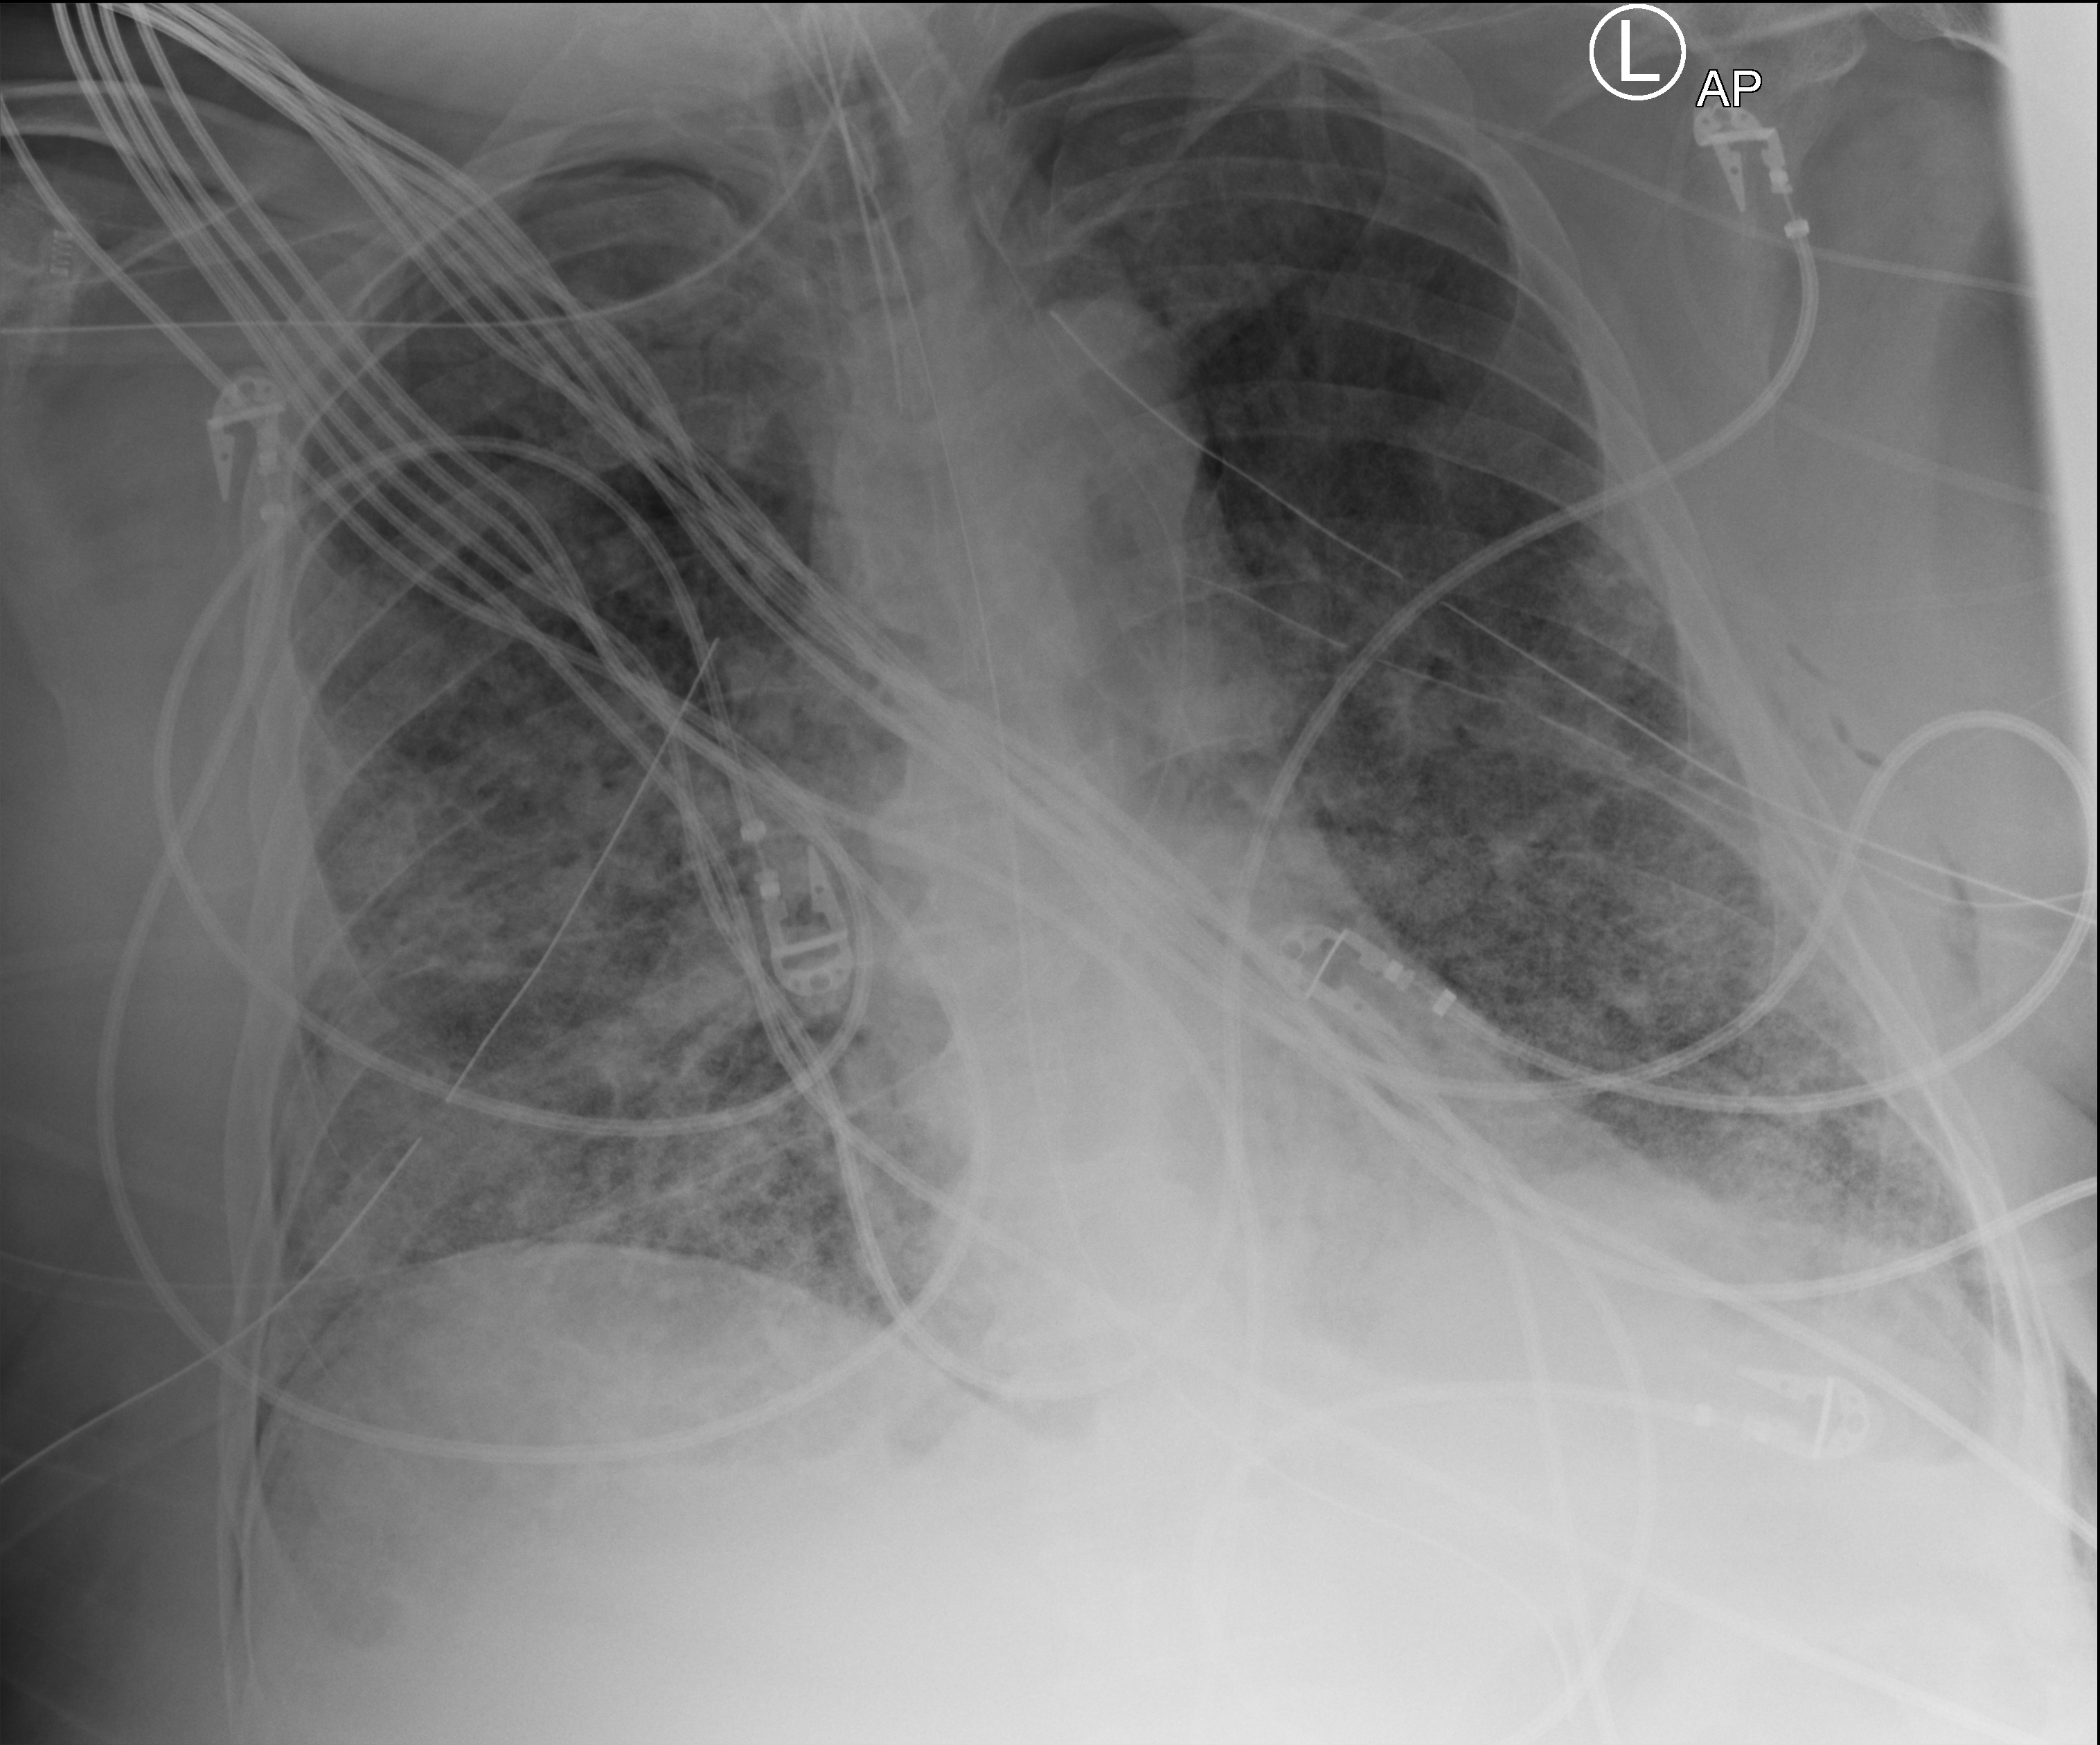
Chest X-ray (portable); anteroposterior (AP) projection. Patient hospitalised with COVID-19, aged 18–59 years.
From the hospital-stay record, not from the radiograph (when in the stay this image was taken is not recorded):
- hypertension (admission record): yes
- admitted to intensive care during this hospital stay: yes
- mechanically ventilated during this hospital stay: yes